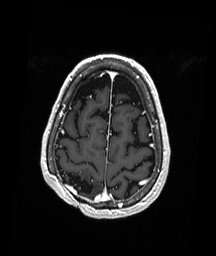
Brain MRI from a brain-tumour surgery series, one axial slice; position 53 of 192 along the scan axis; T1-weighted post-contrast; 1 mm slice thickness; 216 × 256 image matrix, field of view 211 × 250 mm. Case-level facts recorded for this patient, not image findings: histopathology: Astrocytoma; WHO grade: 3; IDH mutation: yes; tumour location: Right Parietal.
Outlined on this slice (outlined manually by an expert reader):
- previous resection cavity: box from (x=63, y=172) to (x=94, y=195) px